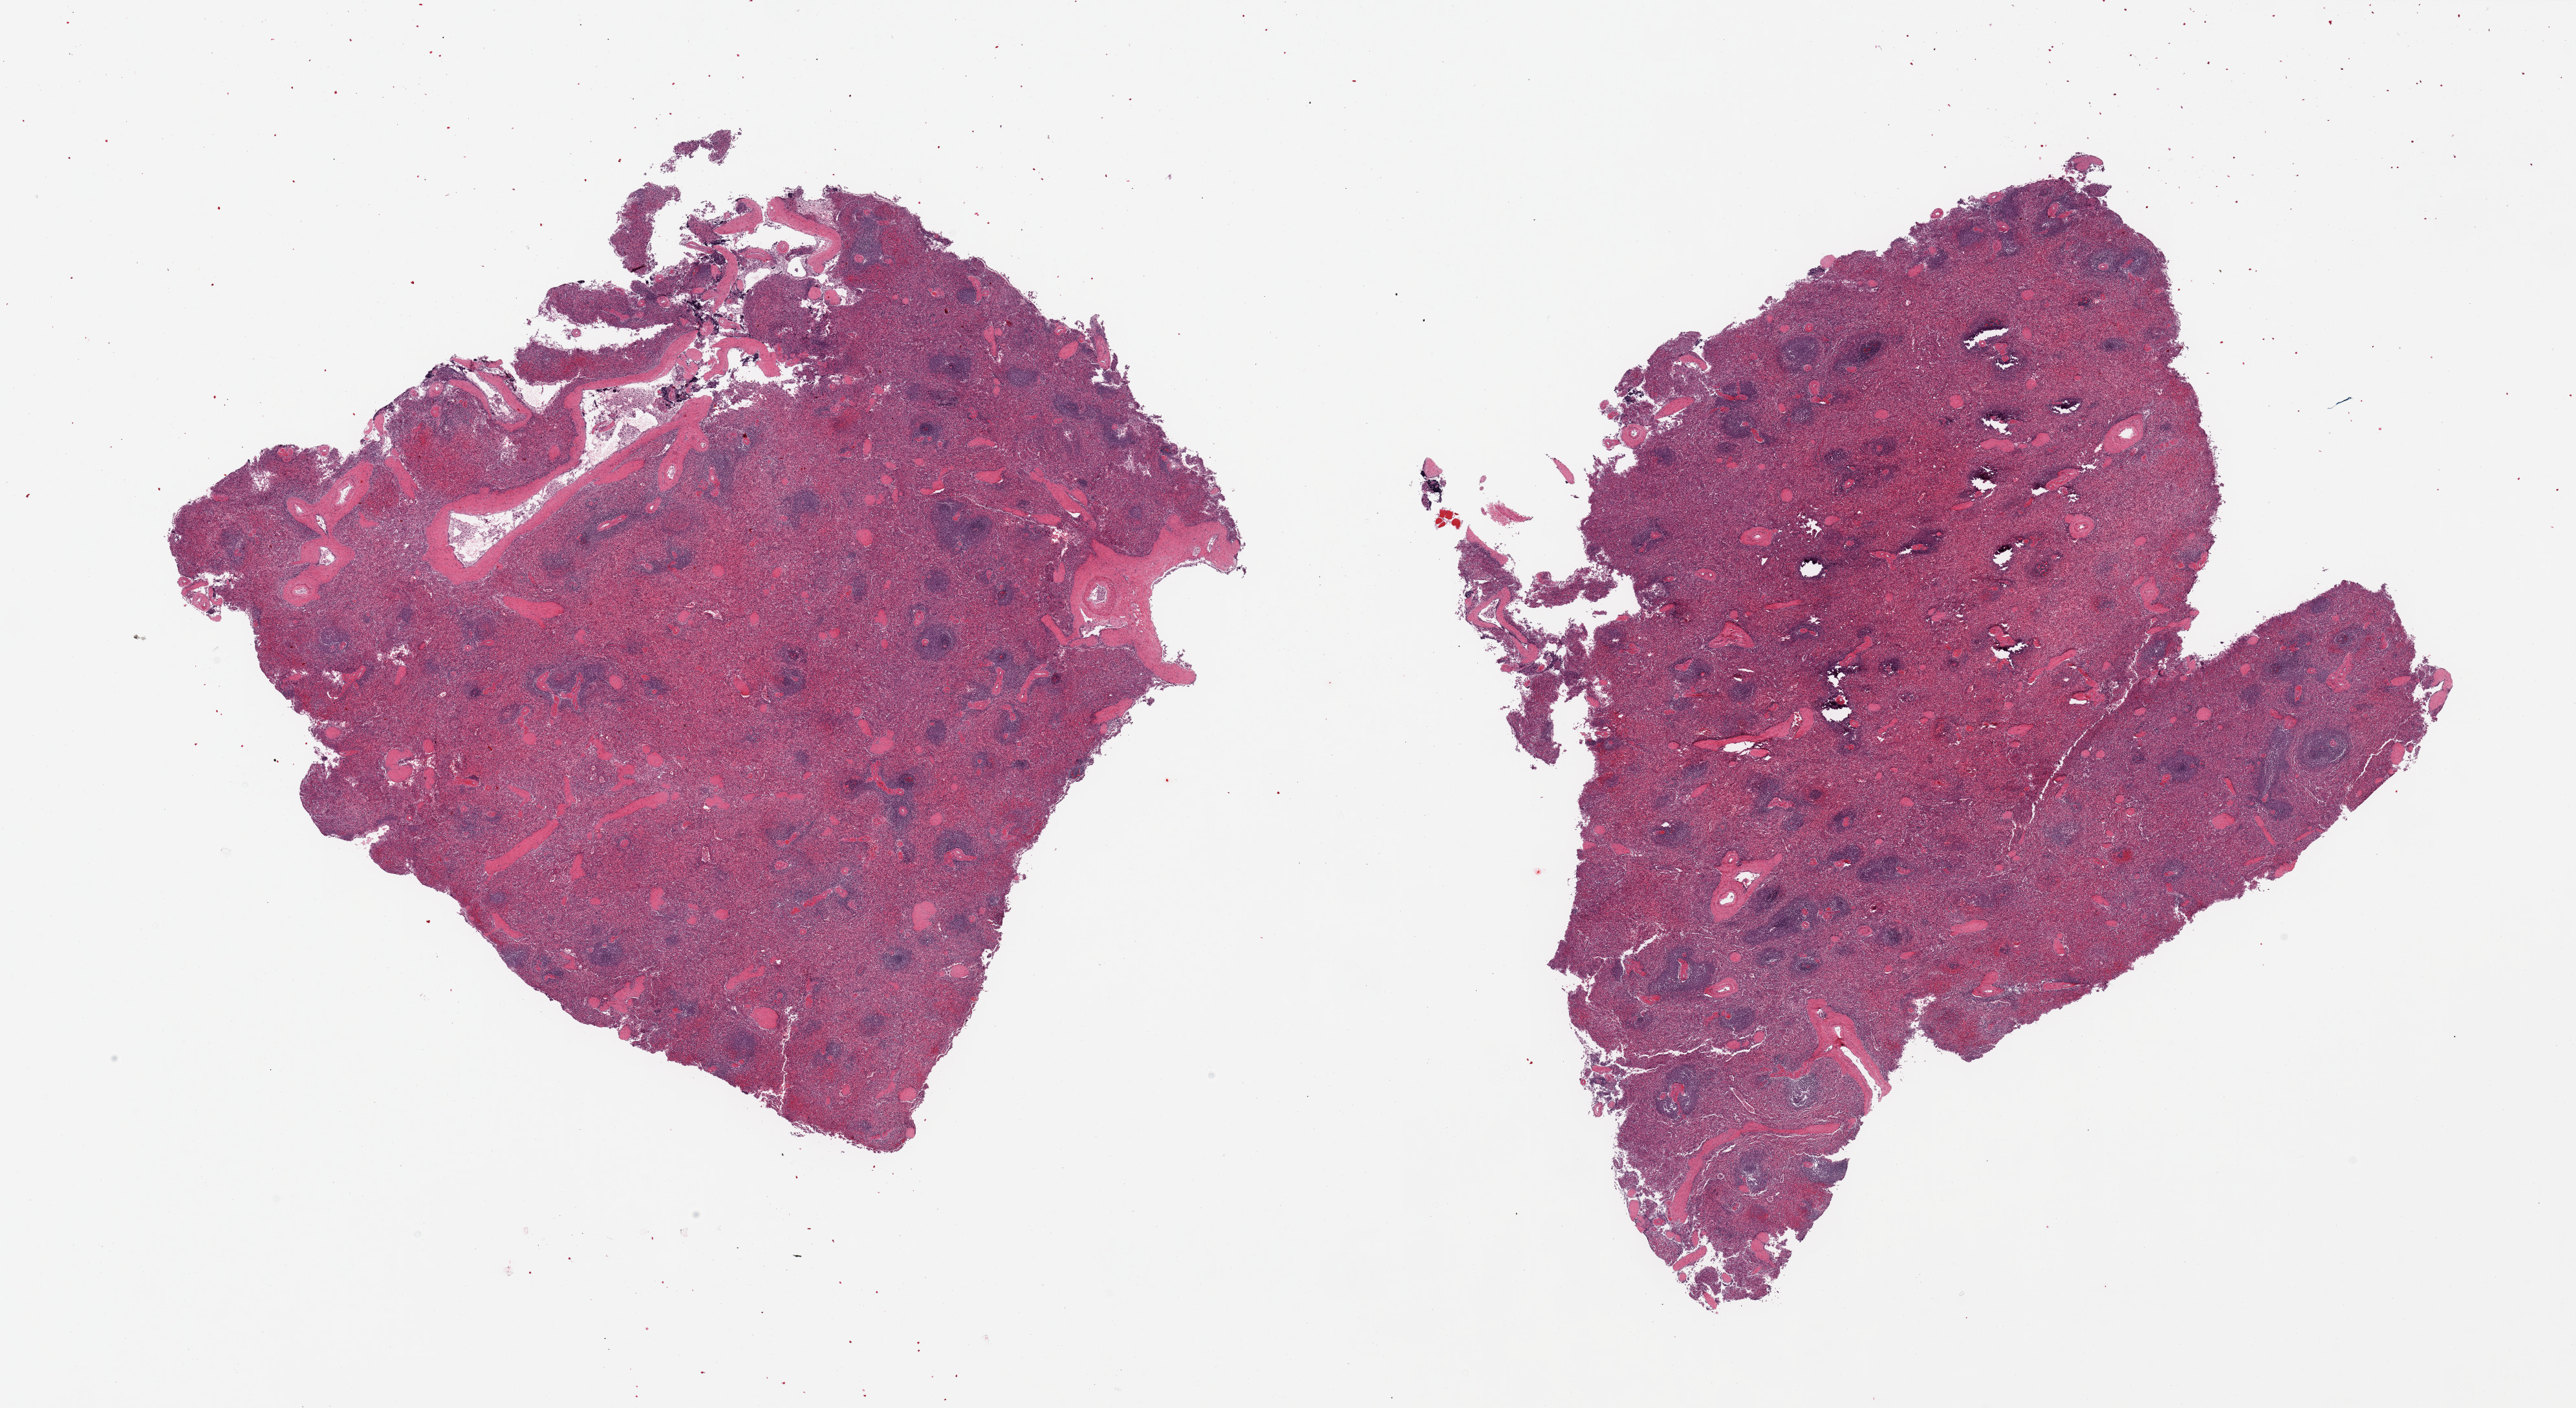
Whole-slide image, H&E stain, brightfield, whole scanned area (about 31.5 x 17.2 mm) shown as a low-resolution overview; PAXgene-fixed paraffin-embedded (PFPE) section; target tissue: spleen; donor tissue sample. Donor sex: male.
Reviewer comment on this tissue sample: 2 pieces.